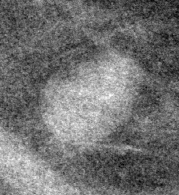
Cropped region of a digitized screen-film mammogram centred on a radiologist-marked abnormality, left breast, CC view.
- Marked abnormality: mass, shape lymph node, margins circumscribed; BI-RADS assessment category 2; benign; no additional work-up was recommended (benign without callback).